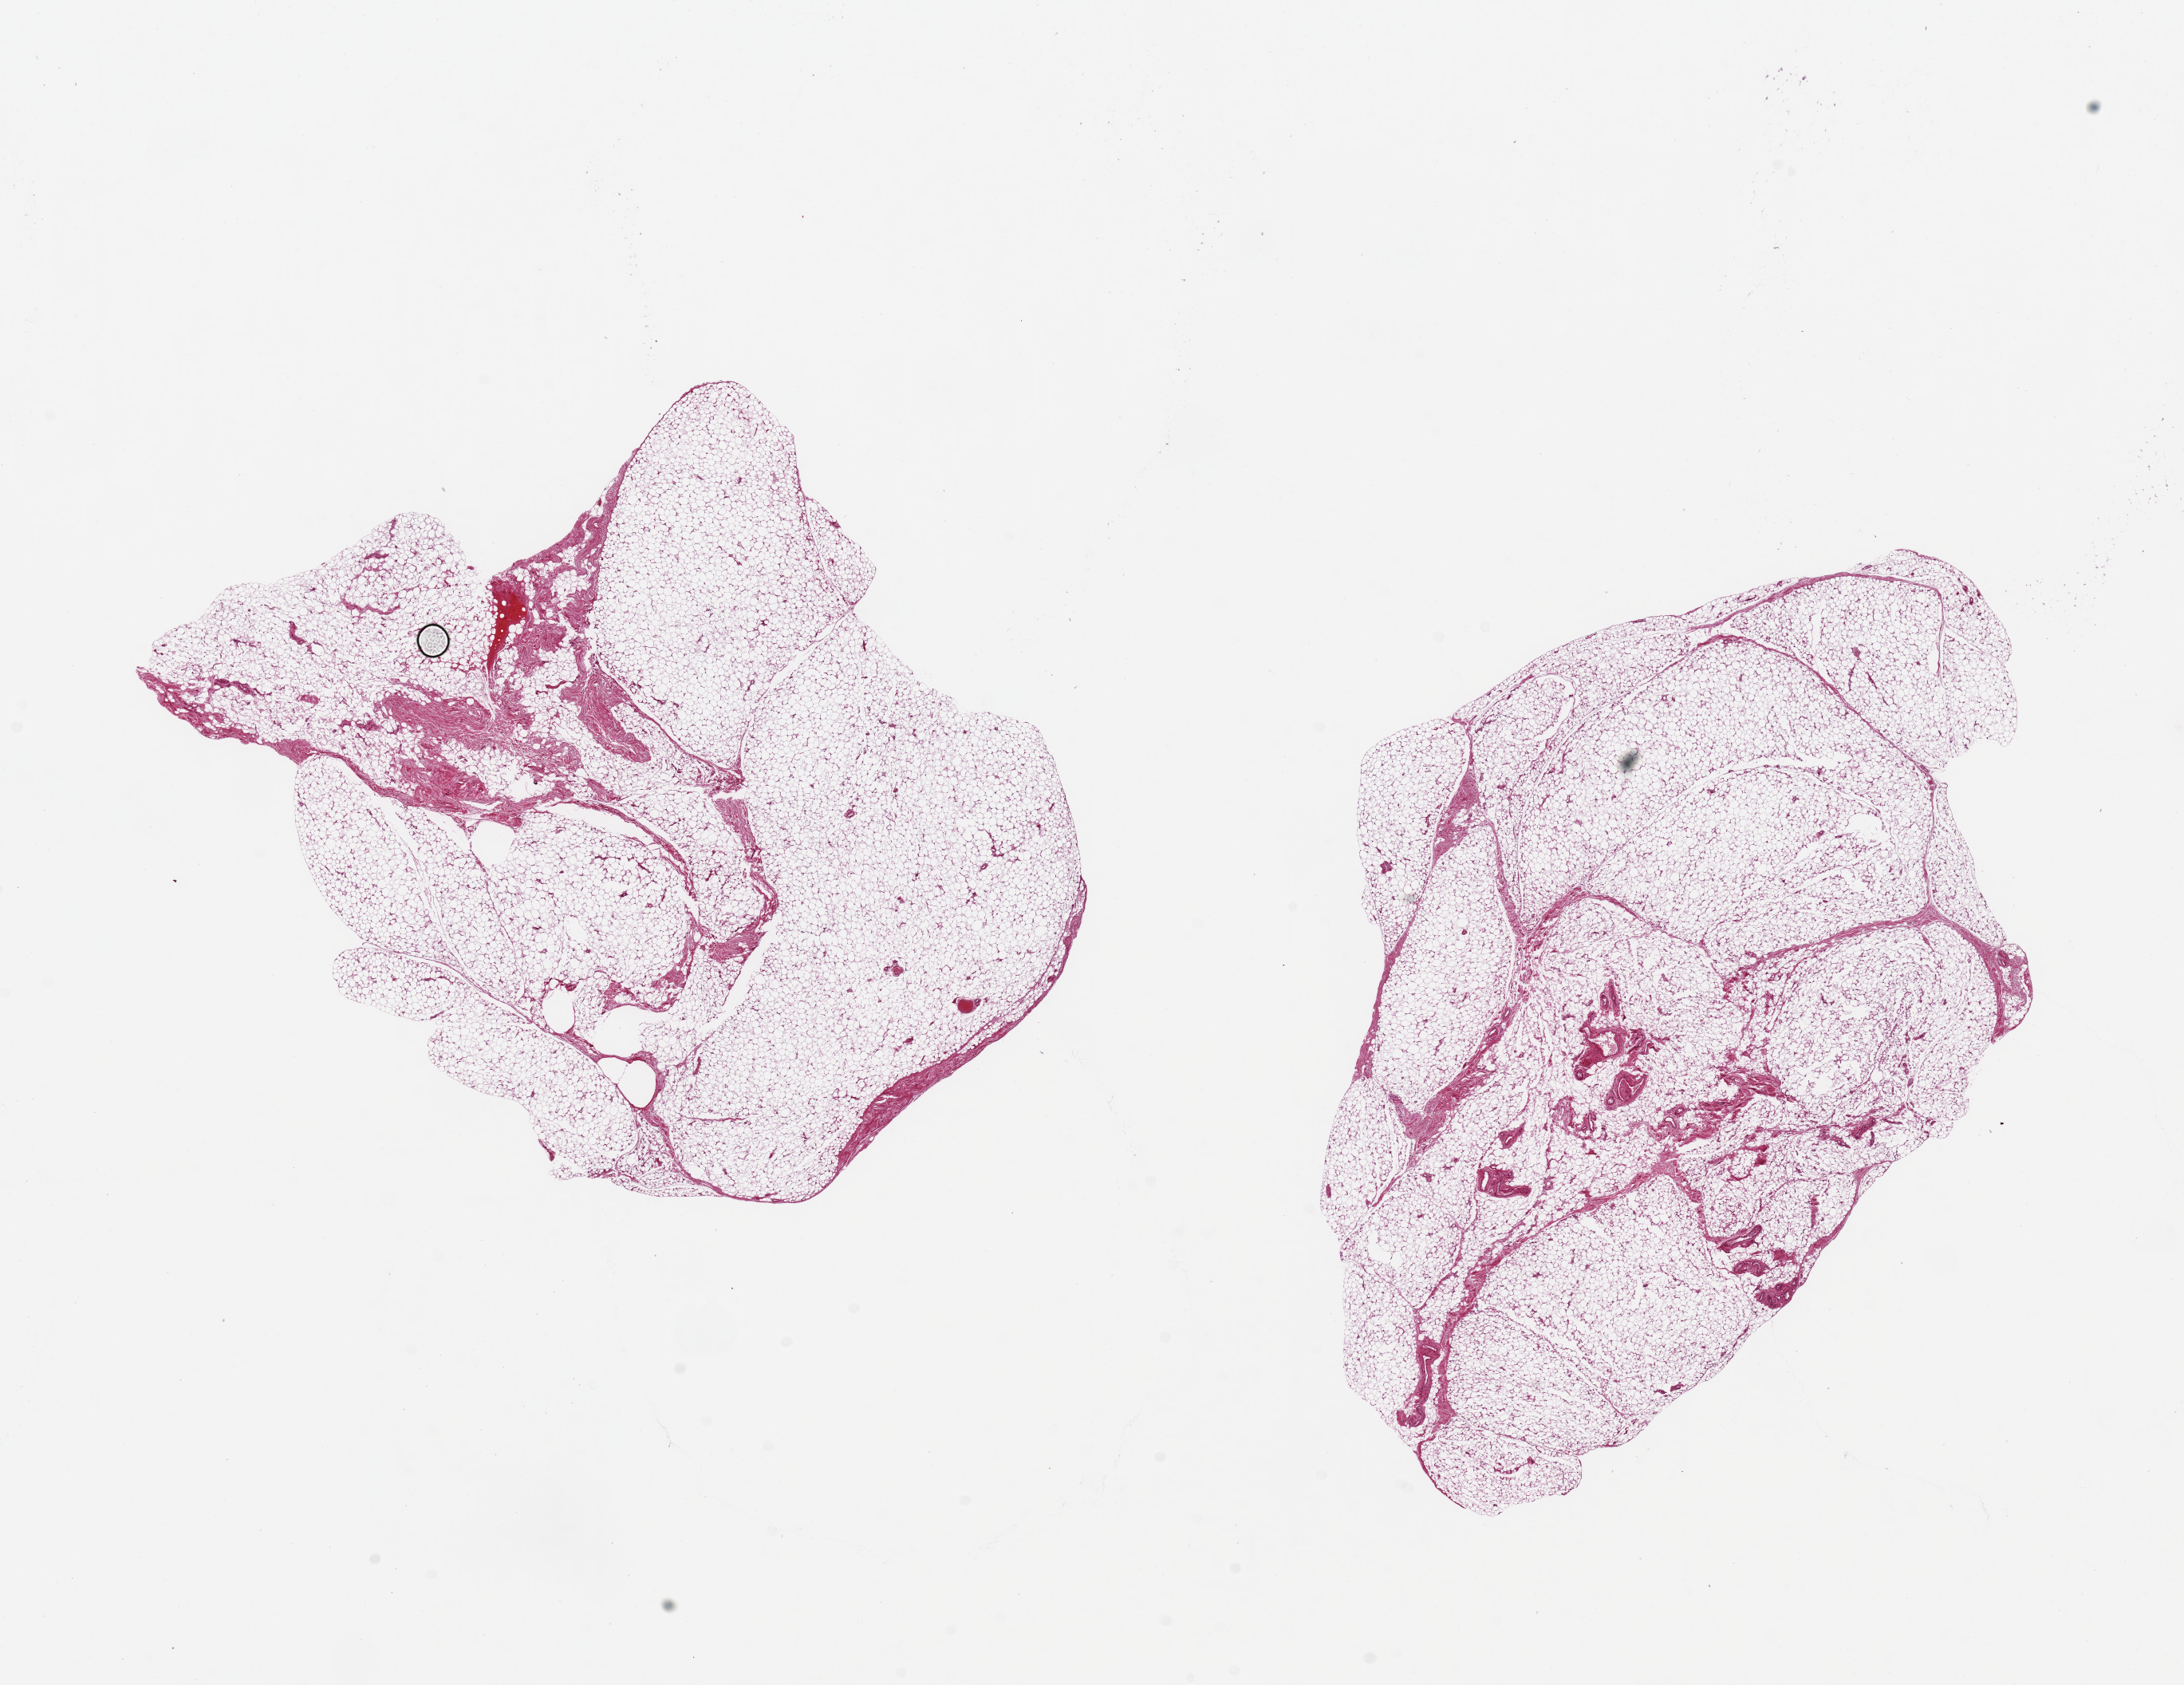
Whole-slide image, H&E stain, brightfield — a low-resolution overview of the entire scanned area, about 21.7 x 16.7 mm. PAXgene-fixed, paraffin-embedded tissue. Target tissue: omentum. Tissue donor sample. Donor sex: male.
Review note (as recorded): 2 pieces, 10x8 & 10x7mm.